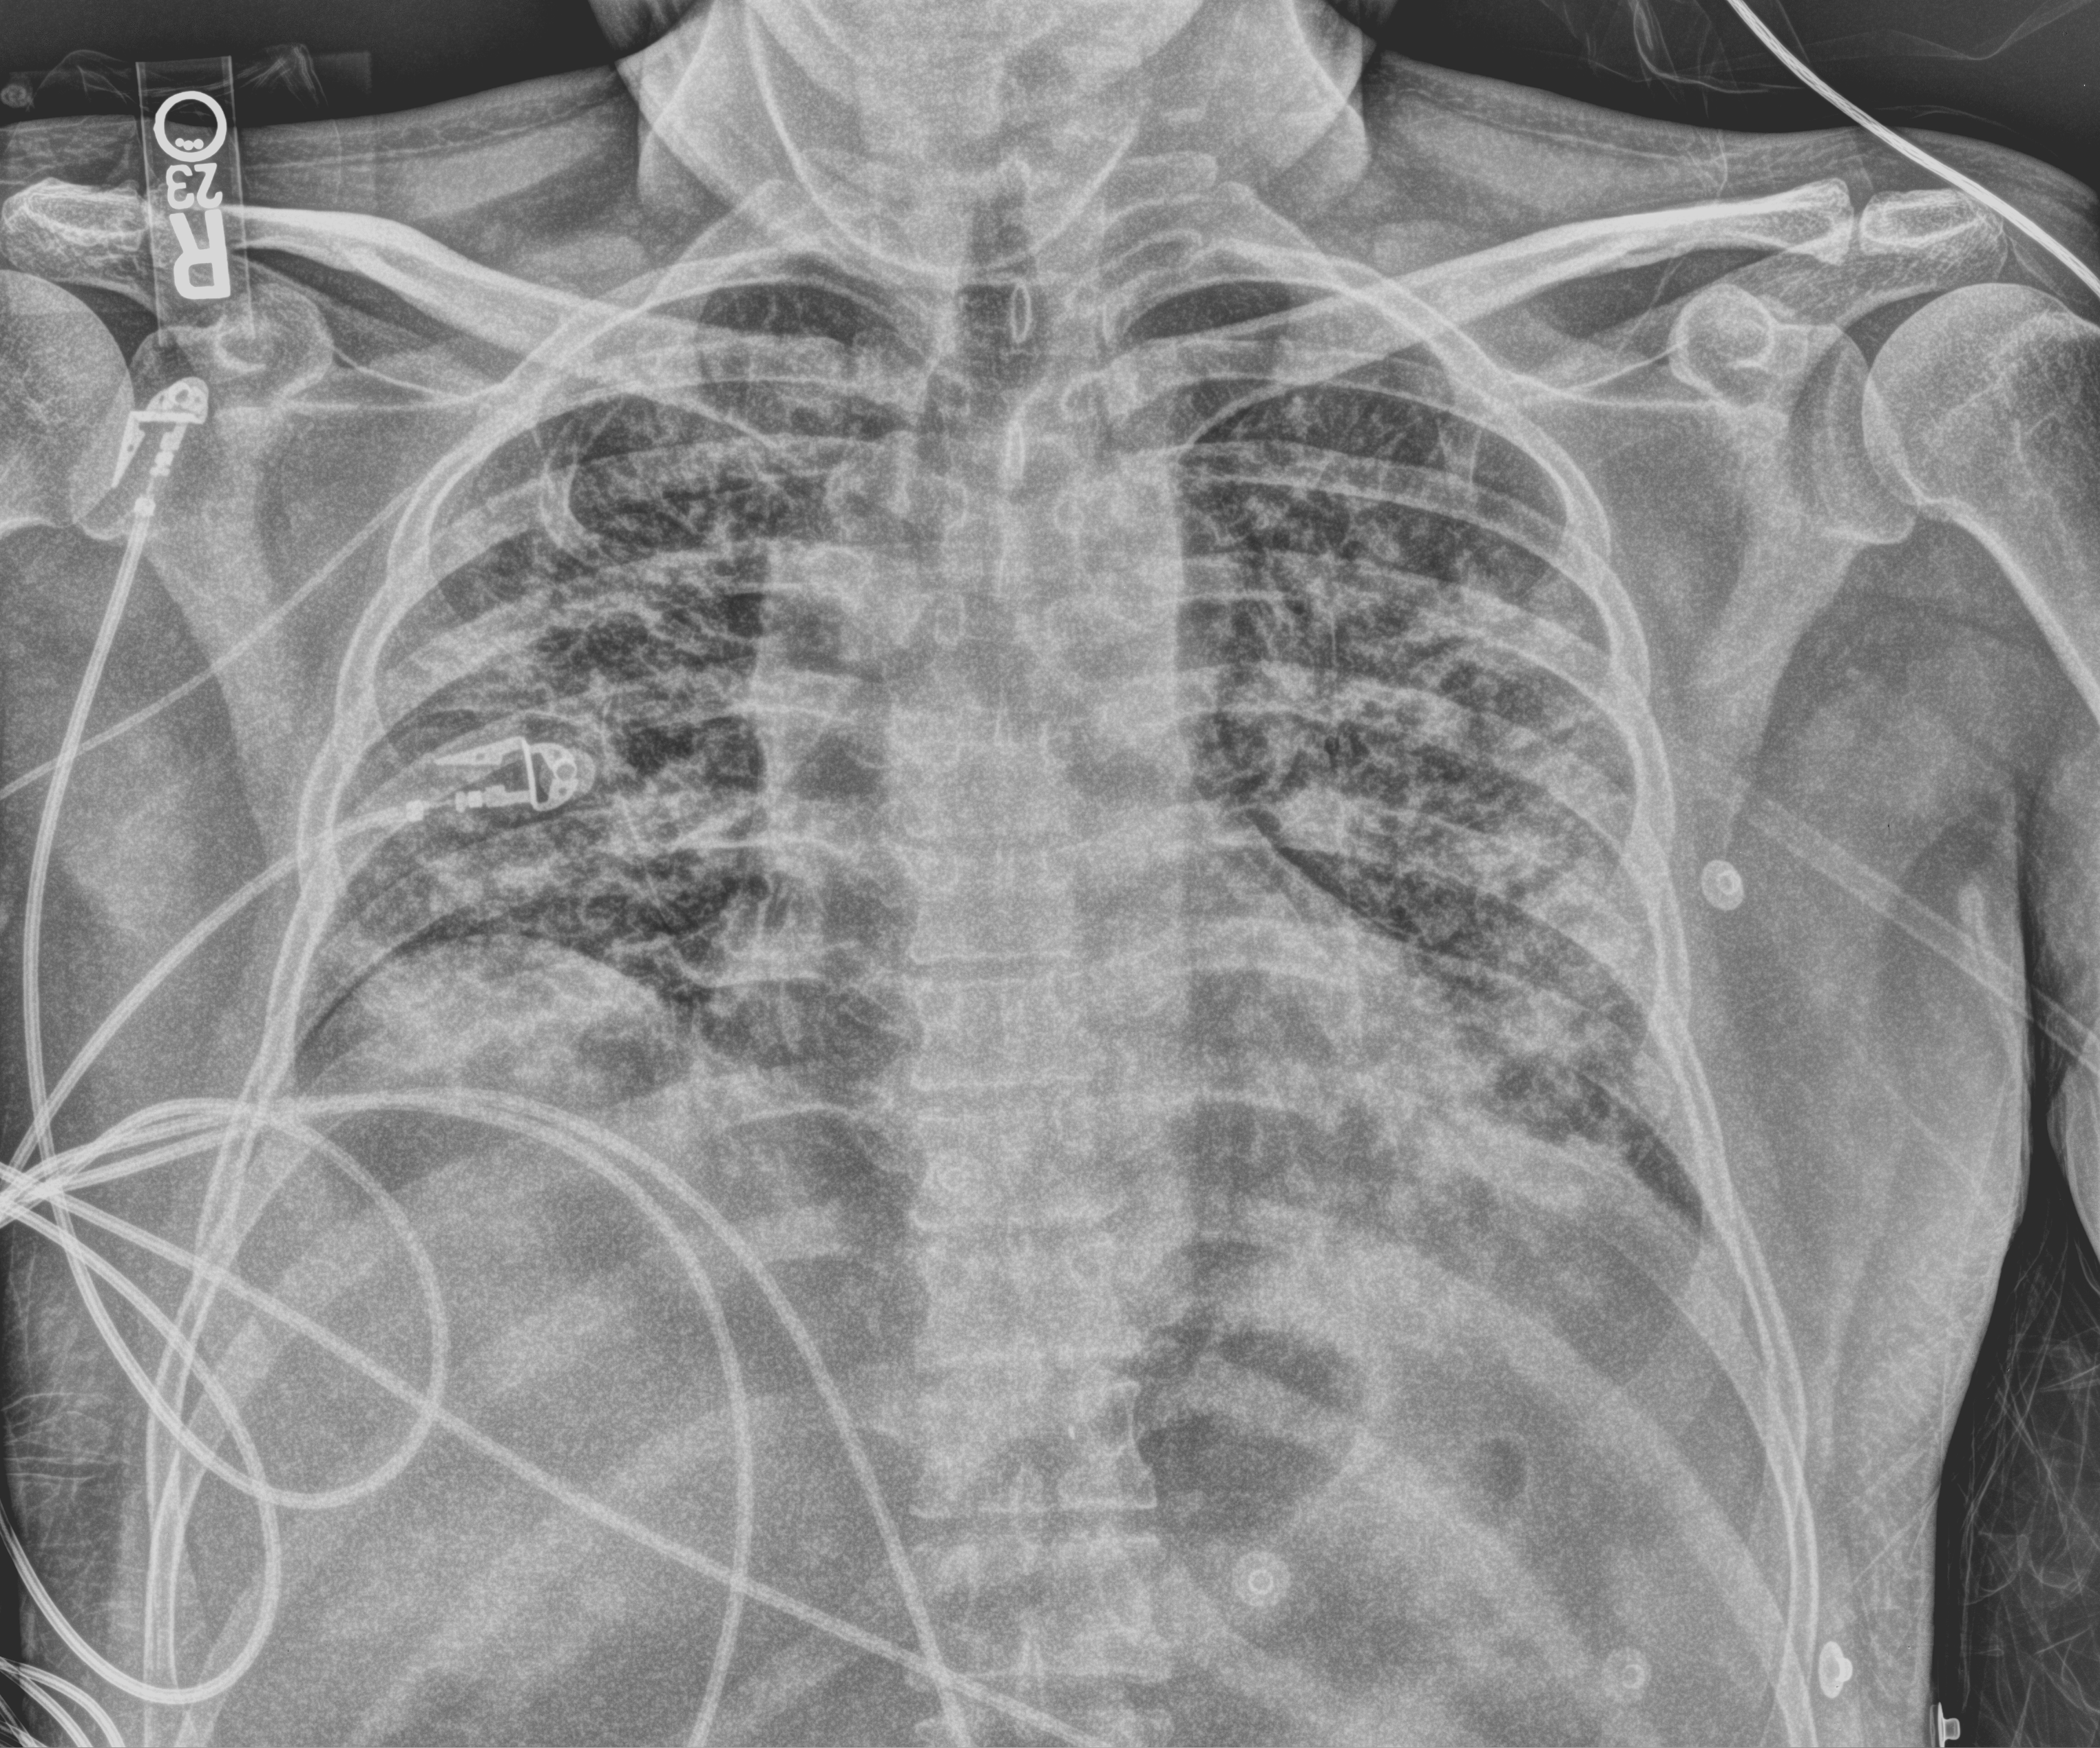
Chest X-ray (portable); anteroposterior (AP) projection. Patient hospitalised with COVID-19; male, aged 18–59 years.
Admission-level facts for this patient (not findings on this image; timing relative to this image not recorded): chronic kidney disease (admission record): no.